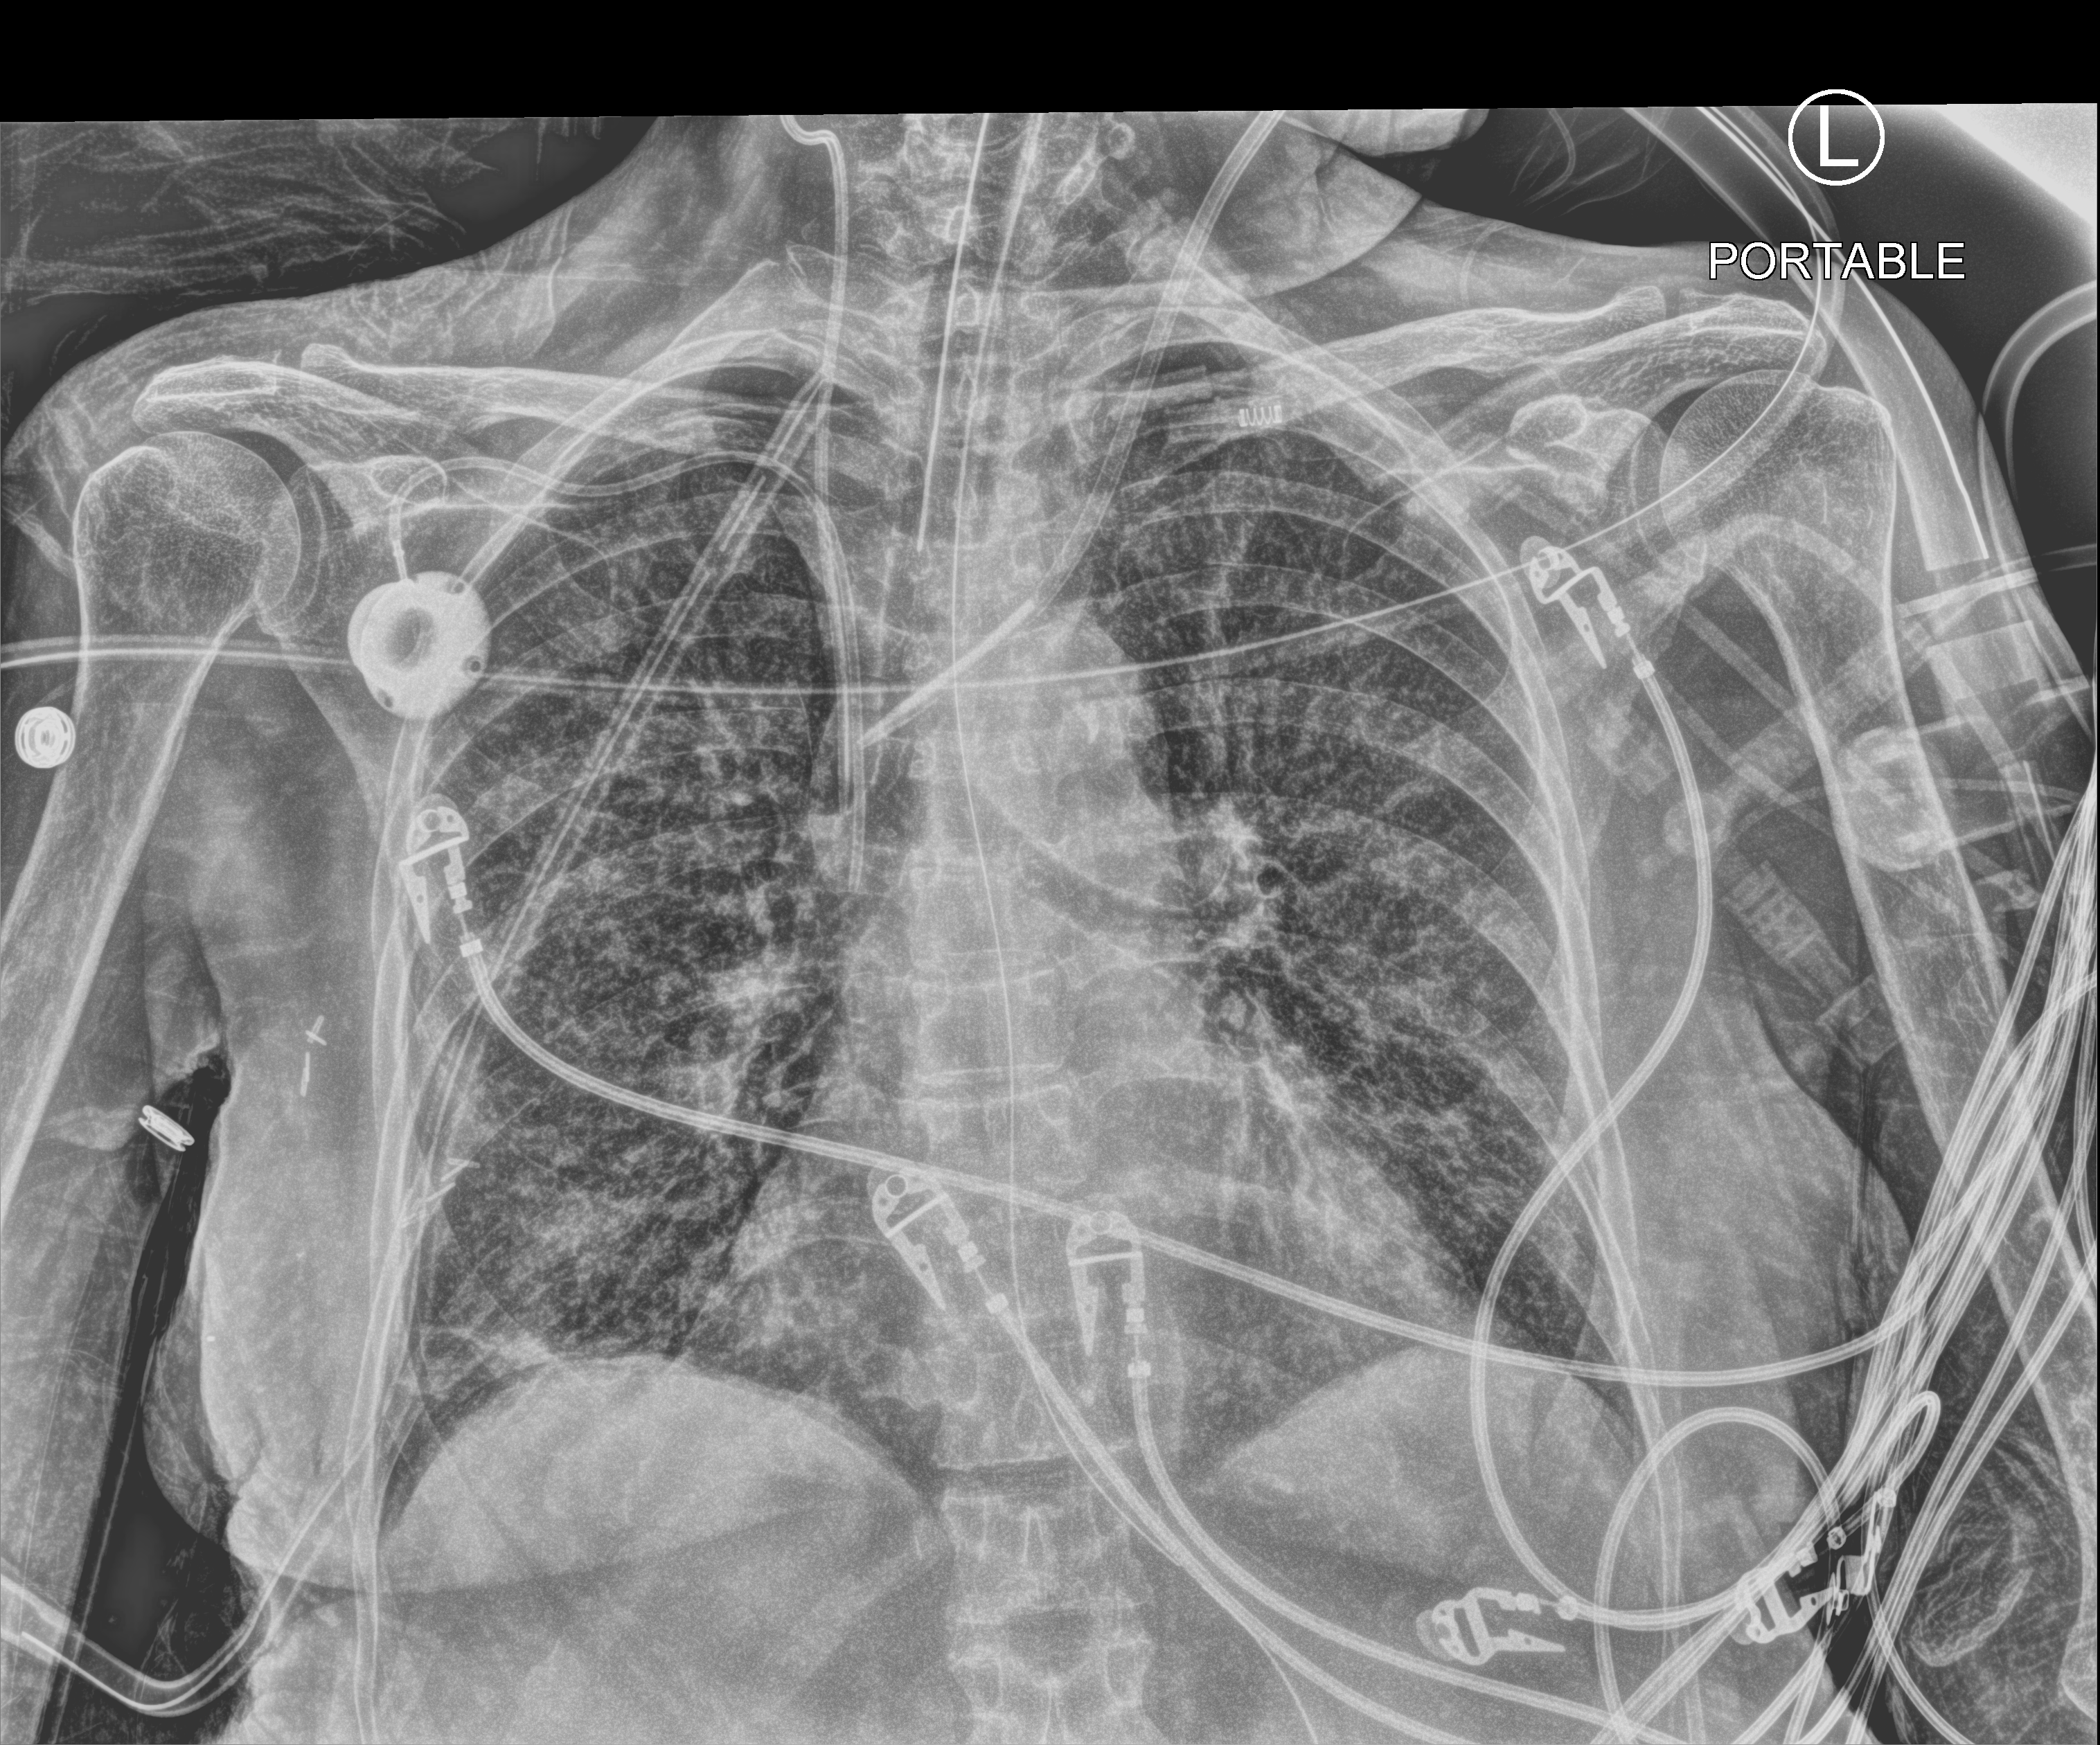
Chest X-ray (portable), anteroposterior (AP) projection. Female patient hospitalised with COVID-19, age 60–74 years.
Hospital-stay facts (about this admission, not read from this image; timing relative to this image not recorded):
- mechanically ventilated during this hospital stay: yes
- admitted to intensive care during this hospital stay: yes
- length of hospital stay: 43 days